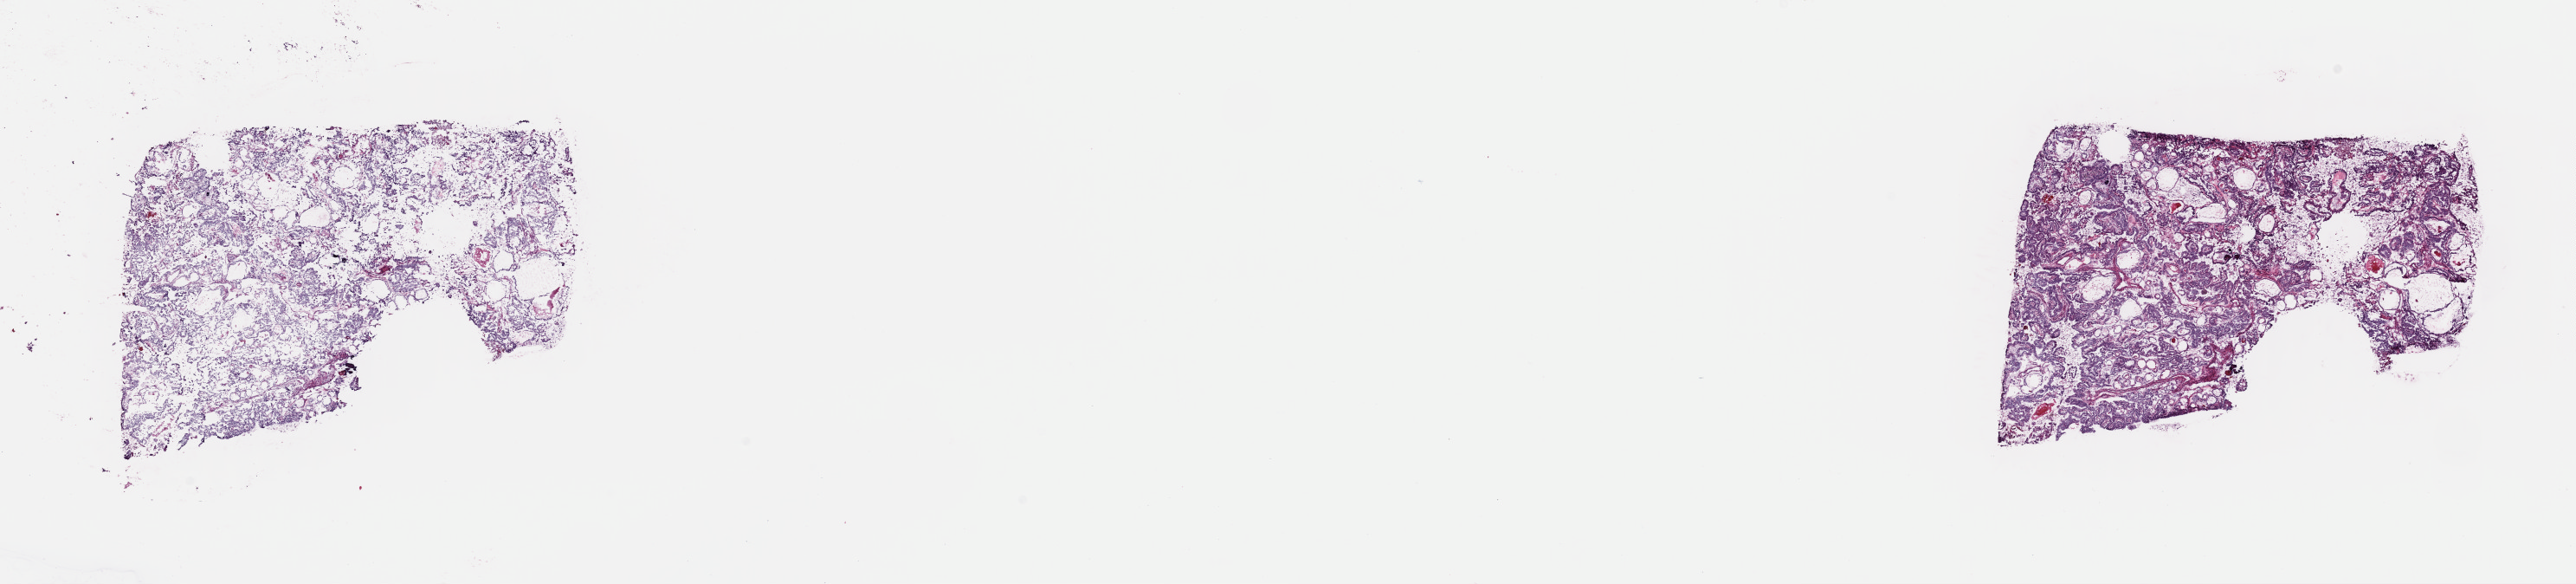
Digitized Hematoxylin and eosin (H&E) stained tissue section (whole slide) — a low-resolution overview of the entire scanned area, about 23.5 x 5.3 mm, frozen section from the top of the tissue portion, sample: primary tumour, thyroid. Female, age 62 years at initial diagnosis.
Pathologic diagnosis: Papillary adenocarcinoma, NOS (thyroid gland).